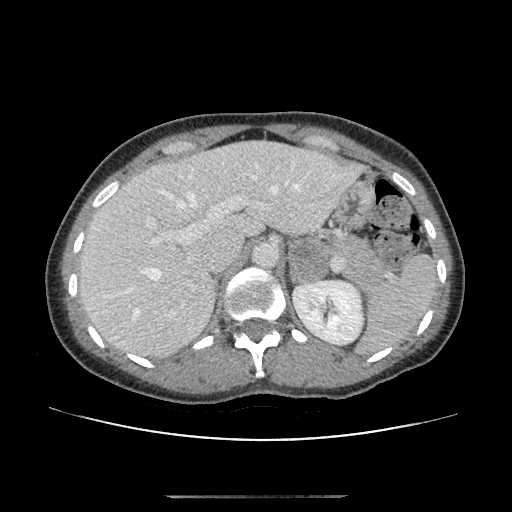
Contrast-enhanced abdominal CT, one axial slice. Position 73 of 179 along the scan axis. Reconstruction kernel STANDARD. Soft-tissue window (W 400 / L 40 HU). 2.5 mm slice thickness. 512 × 512 image matrix. Female patient, age 51 years. From the clinical record (not read from this slice): diagnosis: adrenocortical carcinoma; tumour side: left adrenal; tumour size at pathology: 3.5 cm; Ki-67 index: 45 %; stage (as recorded): 1.
Structures marked on this image (semi-automatically segmented with operator editing):
- mass: bounding box (x1, y1, x2, y2) in pixels: (290, 237, 329, 283)